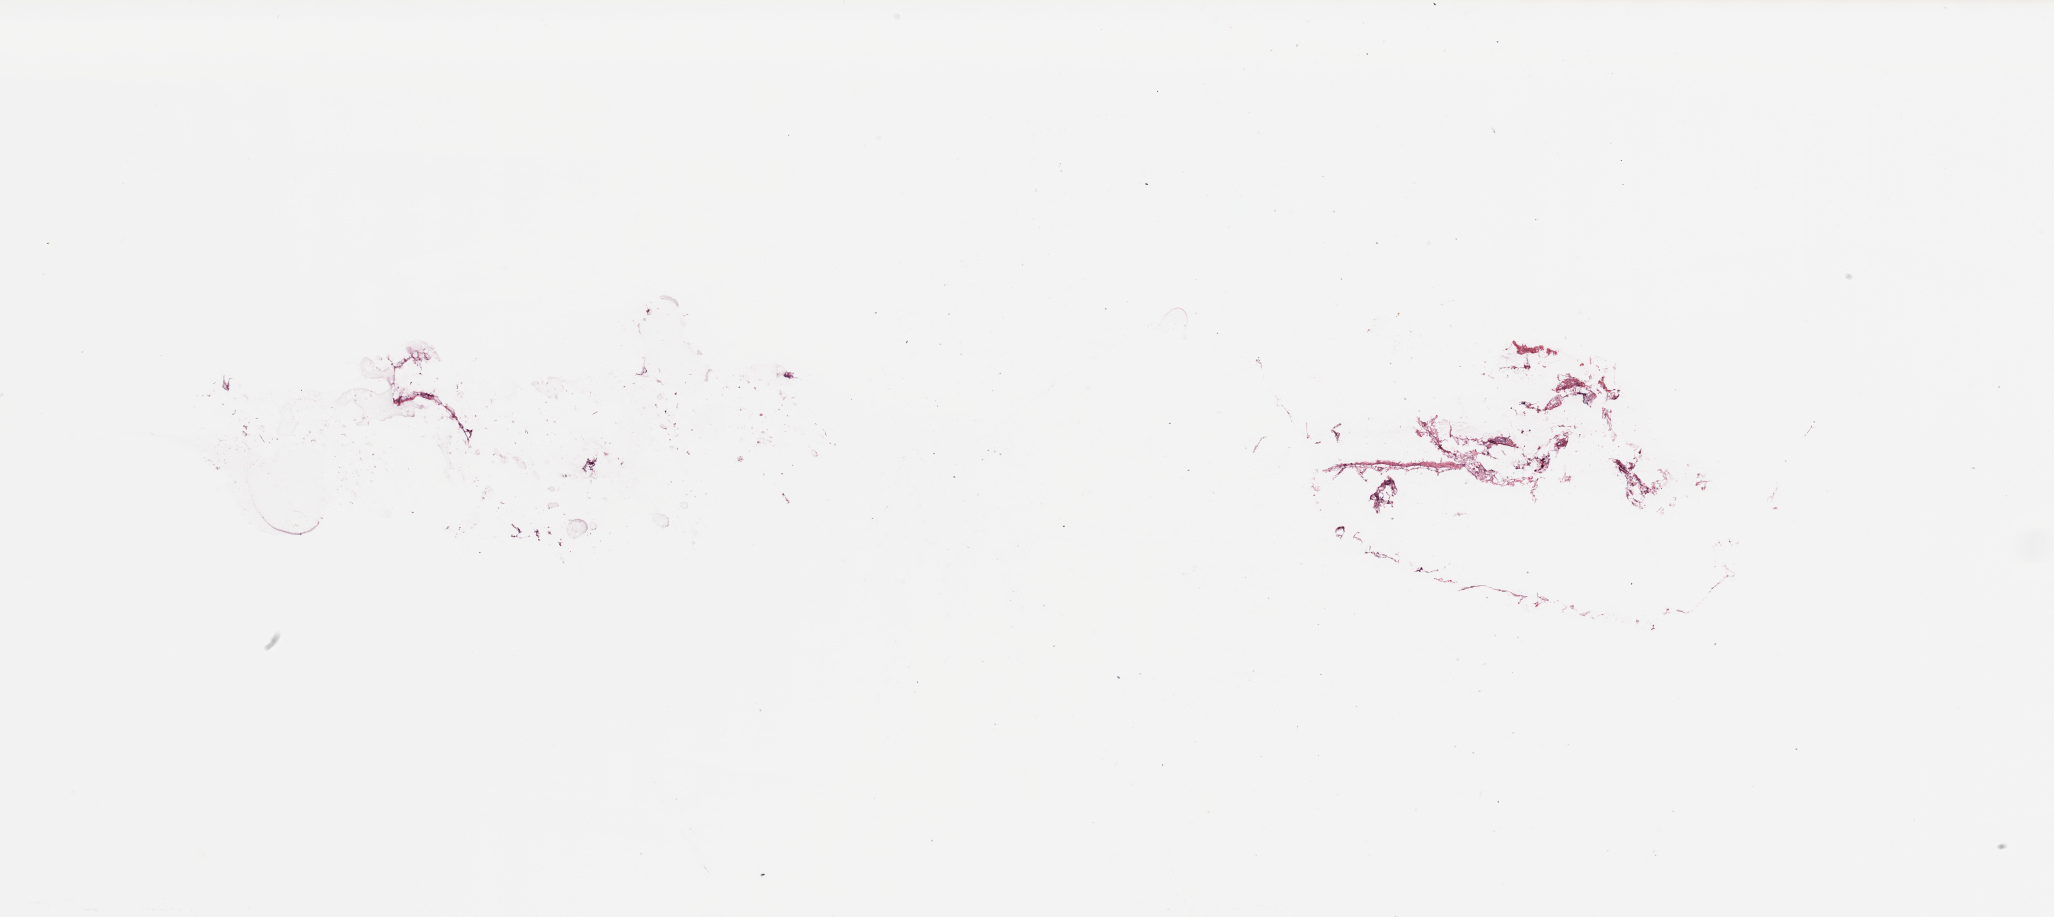
H&E-stained whole-slide image, low-resolution overview of the scanned area, about 32.5 x 14.5 mm (from a 20x scan); breast, tissue type not recorded.
* patient diagnosis (cohort enrolment): breast cancer (breast)